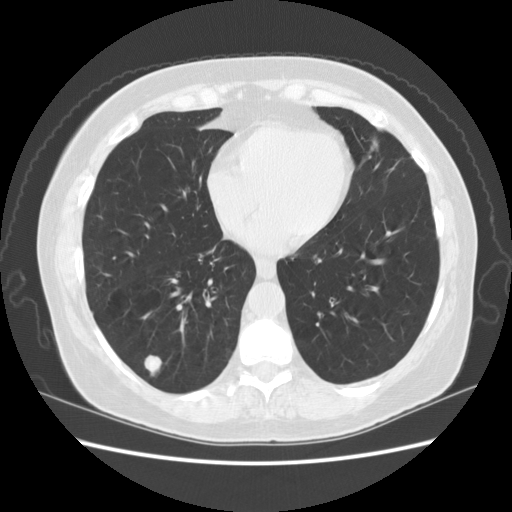
Low-dose screening chest CT, one axial slice. Position 50 of 156 along the scan axis. Reconstruction kernel STANDARD. 120 kVp. Lung window (W 1500 / L -600 HU). 2.5 mm slice thickness. 512 × 512 image matrix, field of view 360 × 360 mm.
Outlined on this slice (expert manual segmentation):
- lesion 1 (tumor, lower lobe of right lung): box from (x=145, y=356) to (x=161, y=374) px